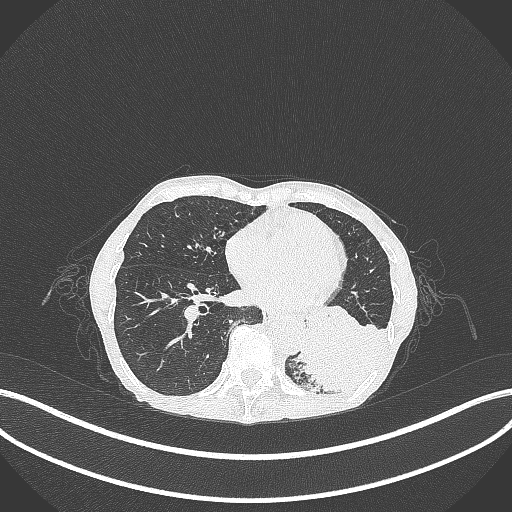
Chest CT, one axial slice. Slice 95 of 347 in the series (ordered by position). Reconstruction kernel B70f. 120 kVp. Lung window (W 1500 / L -600 HU). 1 mm slice thickness. 512 × 512 image matrix, field of view 400 × 400 mm. Female patient, age 70 years. Case-level facts recorded for this patient, not image findings: clinical TNM (as recorded): T3 N0 M0; histopathological grade: G3.
Annotated regions visible in this slice (bounding box drawn by a radiologist):
- lung tumour (recorded histology: small cell carcinoma): box from (x=292, y=319) to (x=388, y=397) px